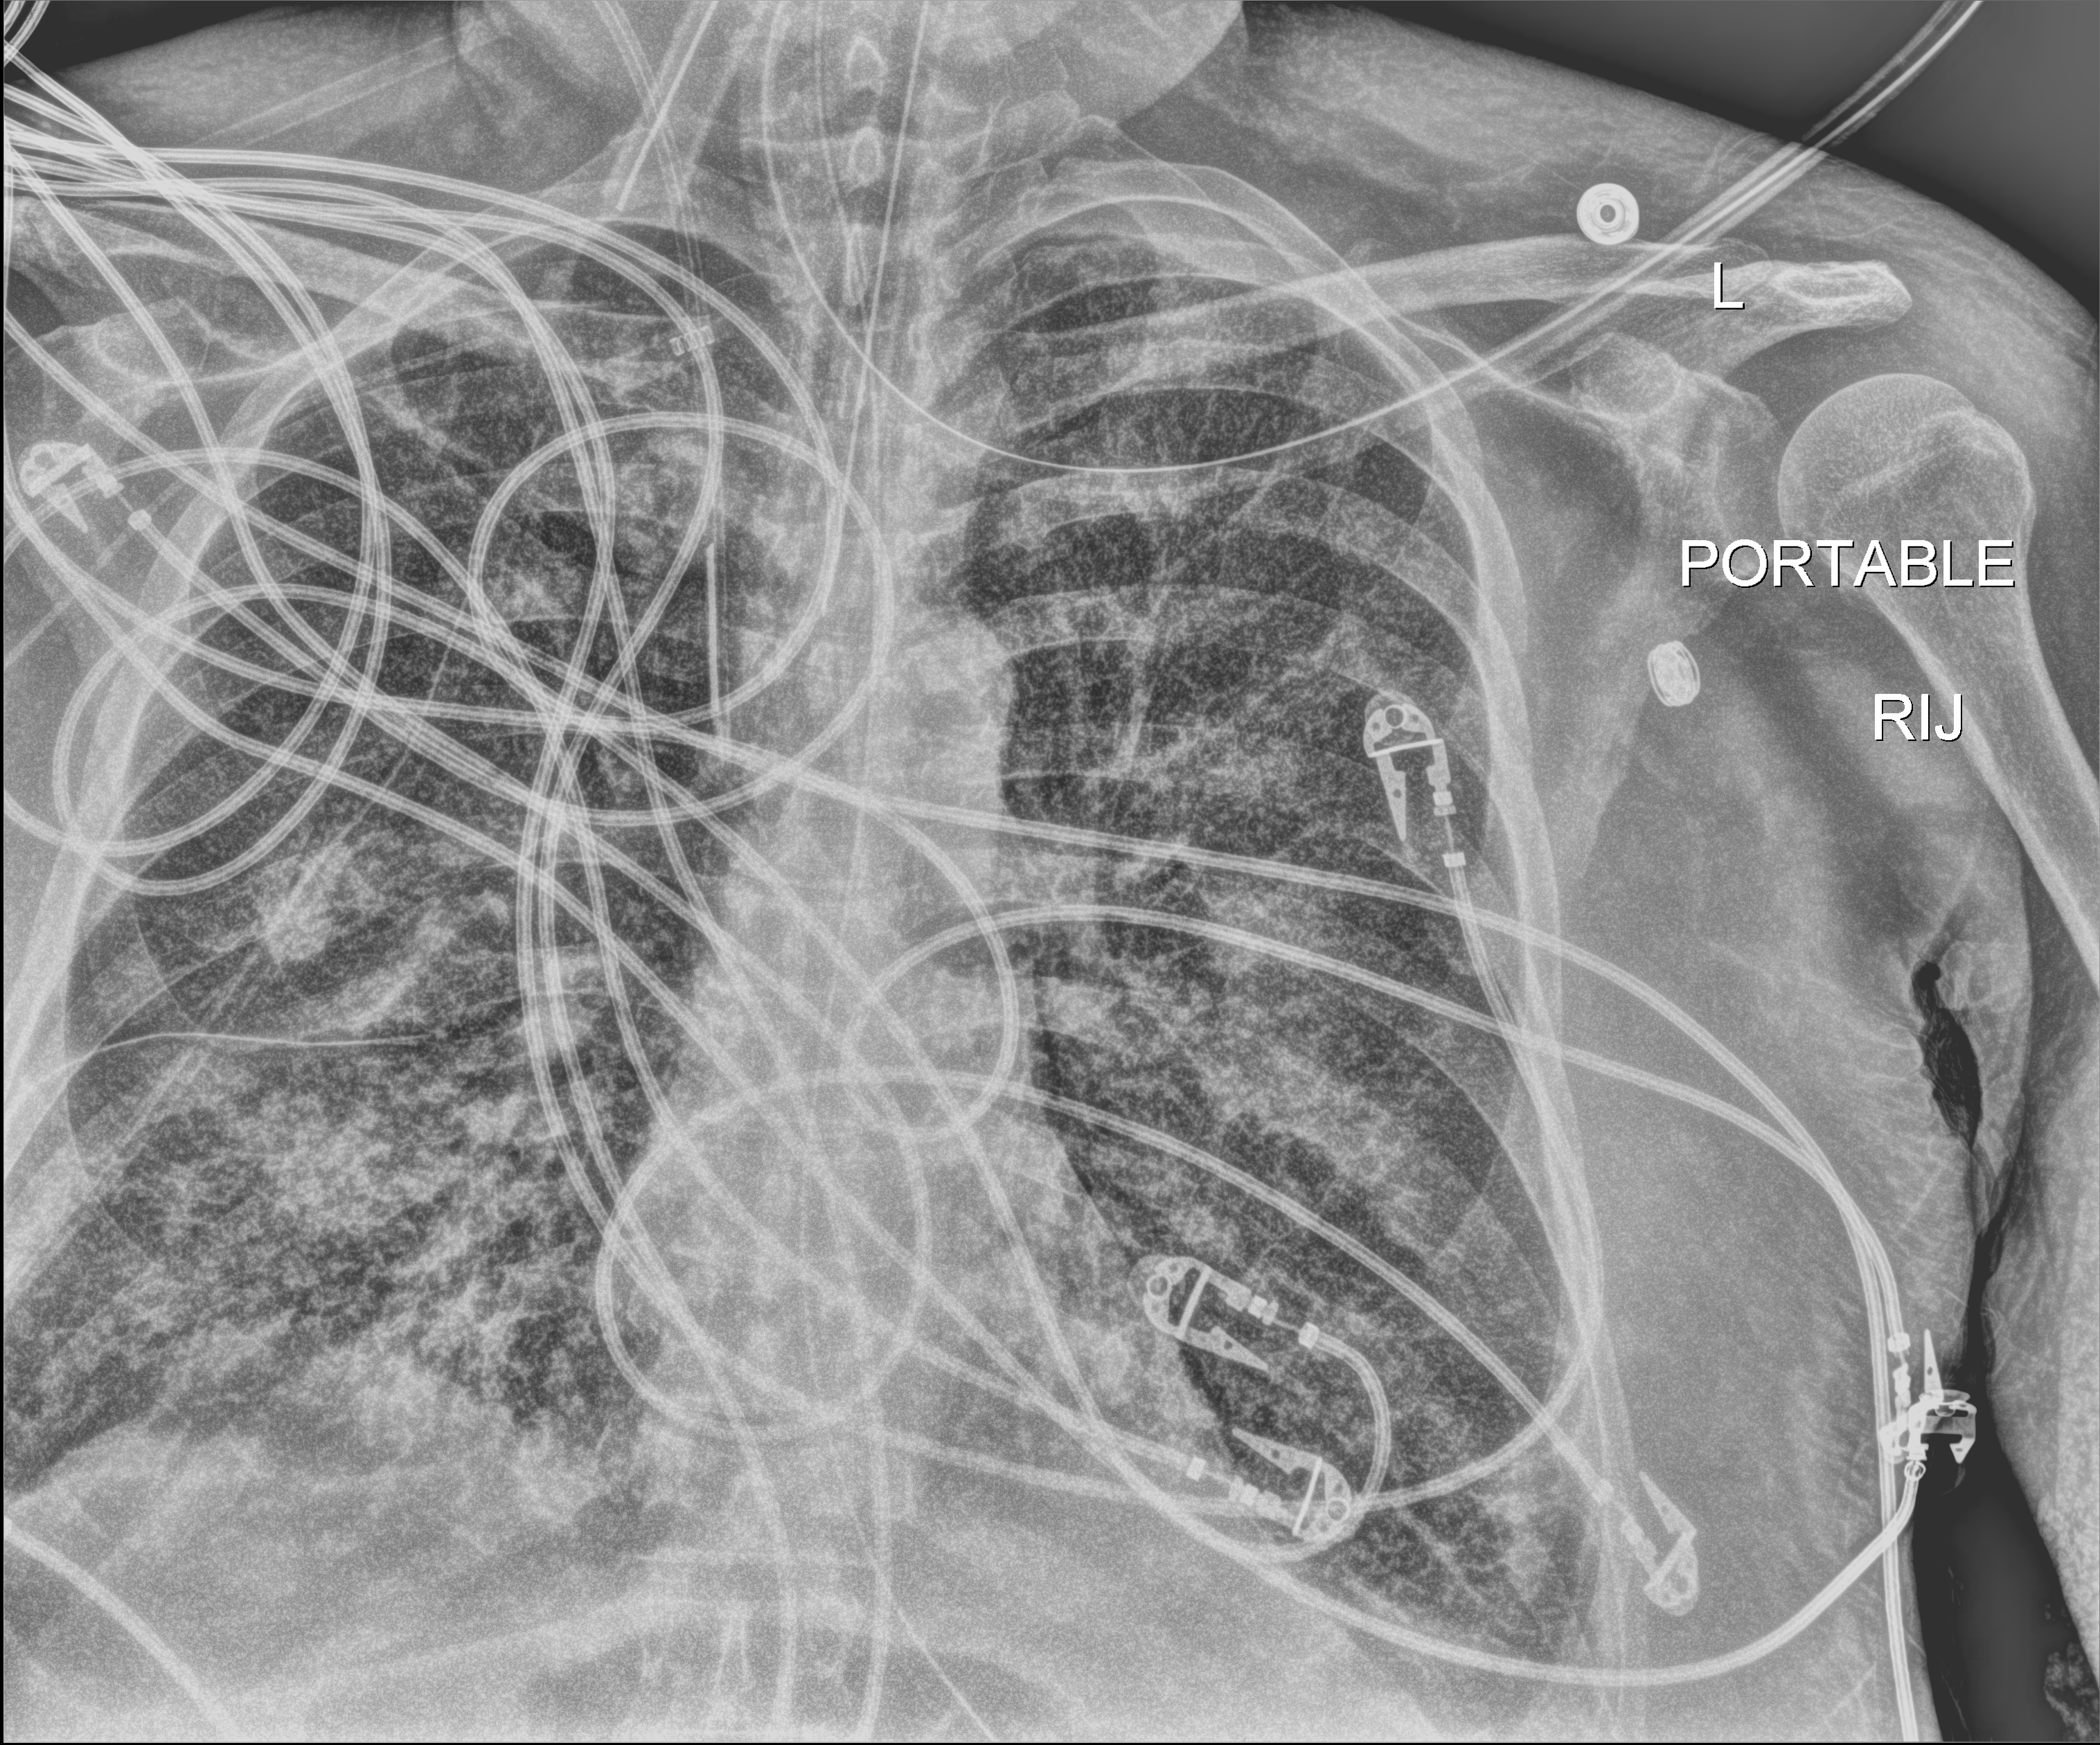
Bedside chest radiograph (digital radiography); anteroposterior (AP) projection. Patient hospitalised with COVID-19; male, aged 60–74 years.
From the hospital-stay record, not from the radiograph (when in the stay this image was taken is not recorded): mechanically ventilated during this hospital stay: yes; length of hospital stay: 24 days.